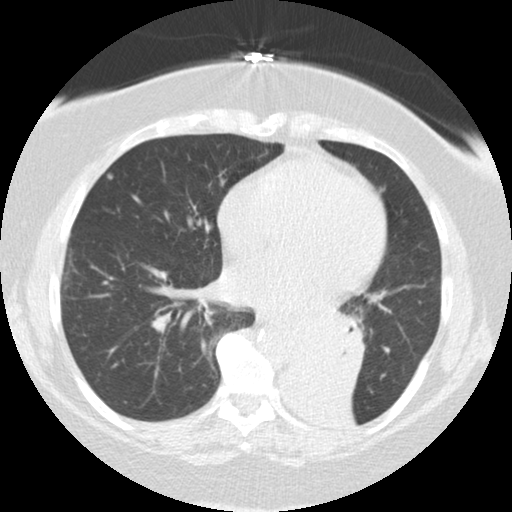
Chest CT (low-dose screening protocol), one axial image. Baseline screening round. Lung window (W 1500 / L -600 HU). 2.5 mm slice thickness. 120 kVp. Slice 75 of 136 in the series. 512 × 512 image matrix. Female, age 71 years at enrolment. Former smoker at enrolment.
Lesion marked by an expert reader, bounding box (x1, y1, x2, y2) in pixels: (281, 303, 368, 383). Reader record for this screening exam (exam-level; its link to the box is not recorded): non-calcified nodule or mass ≥4 mm, right middle lobe, 5 × 5 mm, smooth margins, soft tissue attenuation. Note: the box lies in the patient's left hemithorax on this image, whereas the reader's record names the right lung; they may be different findings. Official screen result: positive, change unspecified: nodule(s) >= 4 mm or enlarging nodule(s), mass(es), or other non-specific abnormalities suspicious for lung cancer. Lung cancer was diagnosed 46 days after this screen: large cell carcinoma, NOS, left lower lobe, mediastinum, other location, poorly differentiated (G3), stage IV (AJCC 6th edition), 50 mm at pathology.